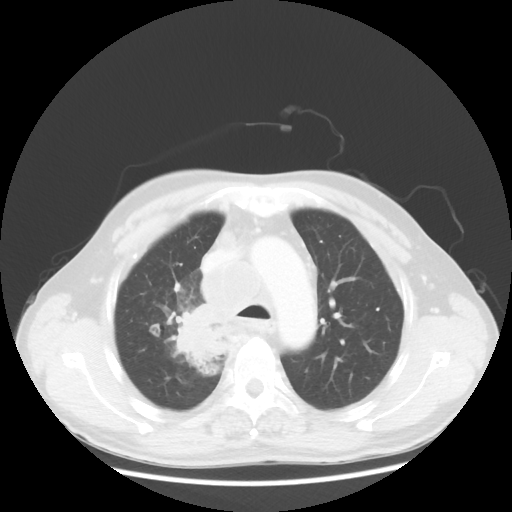
Chest CT, one axial slice. Position 90 of 124 along the scan axis. Reconstruction kernel STANDARD. Lung window (W 1500 / L -600 HU). 512 × 512 image matrix, field of view 382 × 382 mm. Patient: male, 64 years. From the clinical record (not read from this slice): clinical TNM (as recorded): T3 N3 M0; histopathological grade: G3.
Structures marked on this image (rectangle marked by the reading radiologist):
- lung tumour (recorded histology: small cell carcinoma): bounding box [x1, y1, x2, y2] px = [172, 301, 231, 376]